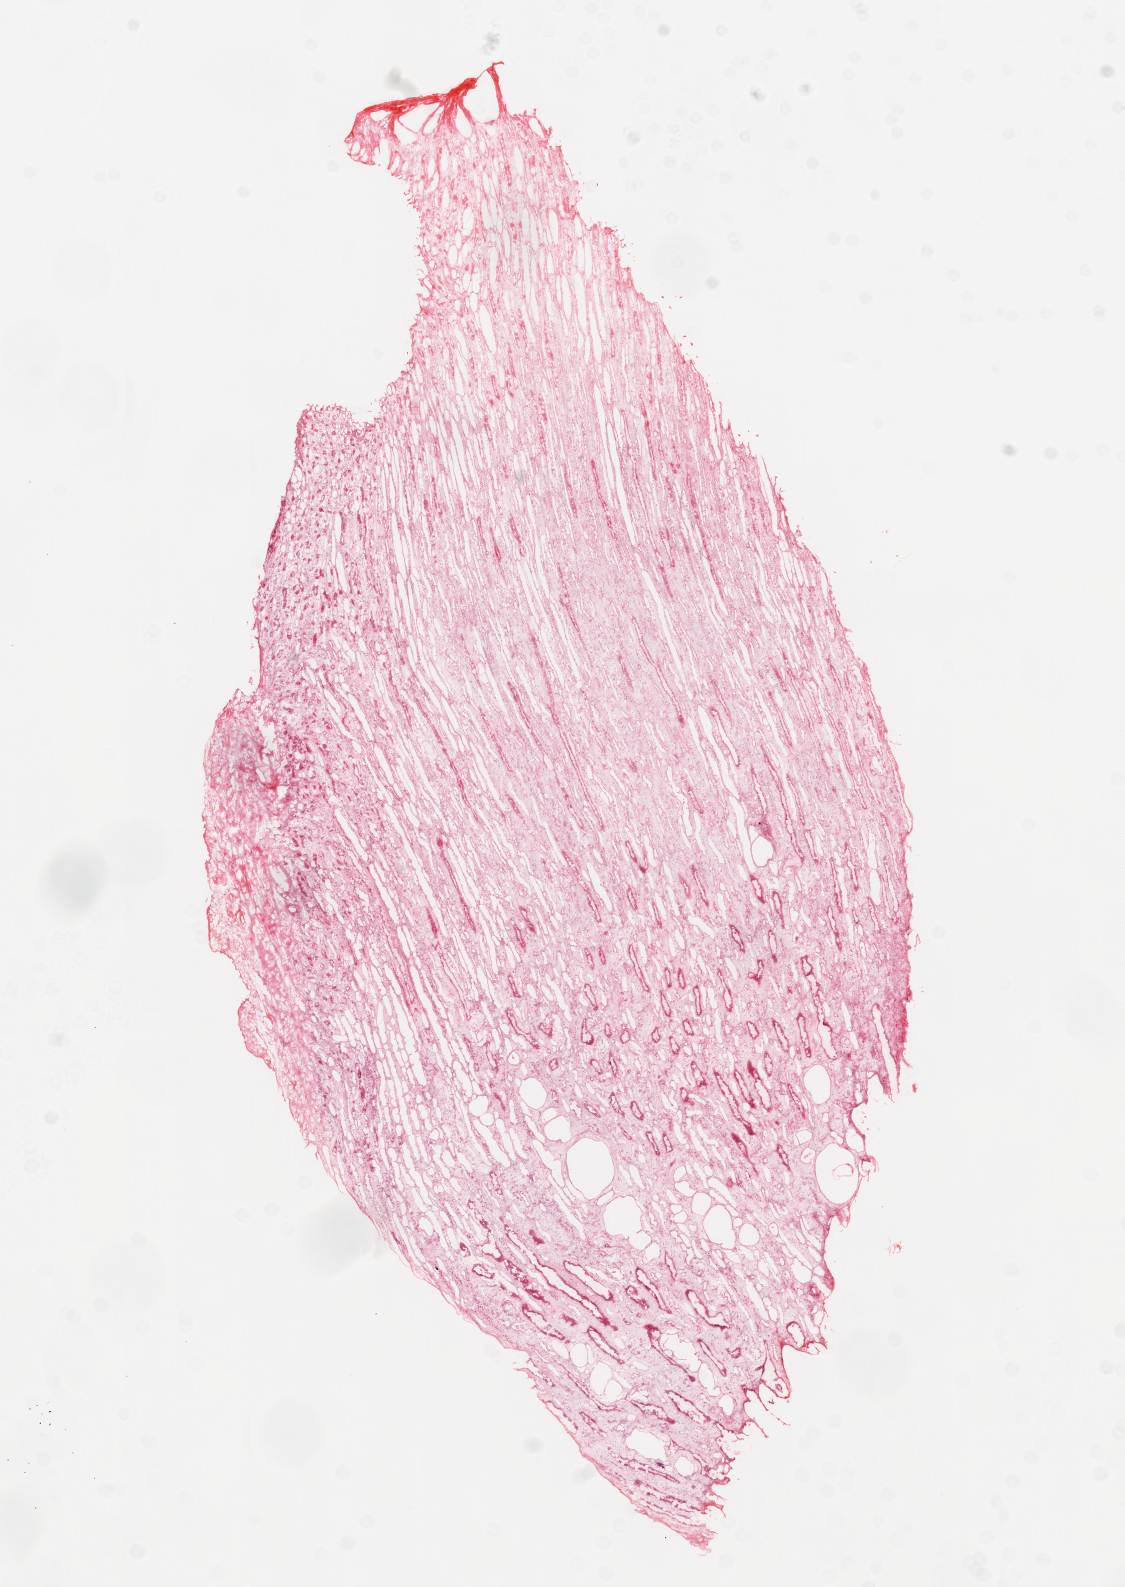
H&E whole-slide image, low-resolution overview of the scanned area, about 9.0 x 12.7 mm (acquisition: 20x scan); frozen section; sample: solid tissue normal (non-tumour tissue), kidney. Female patient; age at initial diagnosis 51 years.
This section: solid tissue normal sample (biorepository sample class). Patient diagnosis: Clear cell adenocarcinoma, NOS.